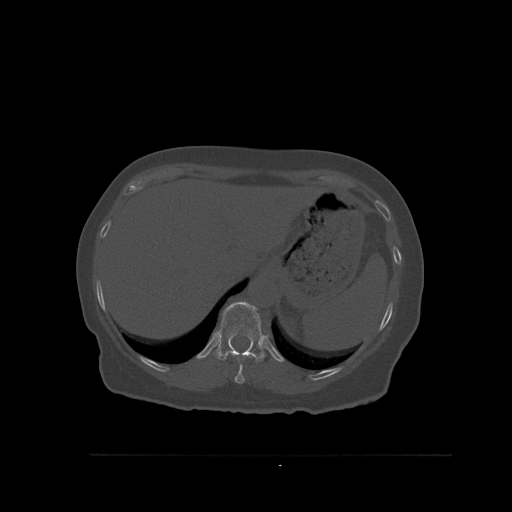
CT including the spine, one axial slice. Position 306 of 527 along the scan axis. Bone window (W 1800 / L 400 HU). 1.5 mm slice thickness. 512 × 512 image matrix. Female patient, age 73 years. Case-level facts recorded for this patient, not image findings: primary cancer: breast.
Structures marked on this image (semi-automatic segmentation, software-assisted and operator-edited):
- T10 vertebra: bounding box <234,356,254,384> (left, top, right, bottom; pixels)
- T11 vertebra: <213,301,266,362>